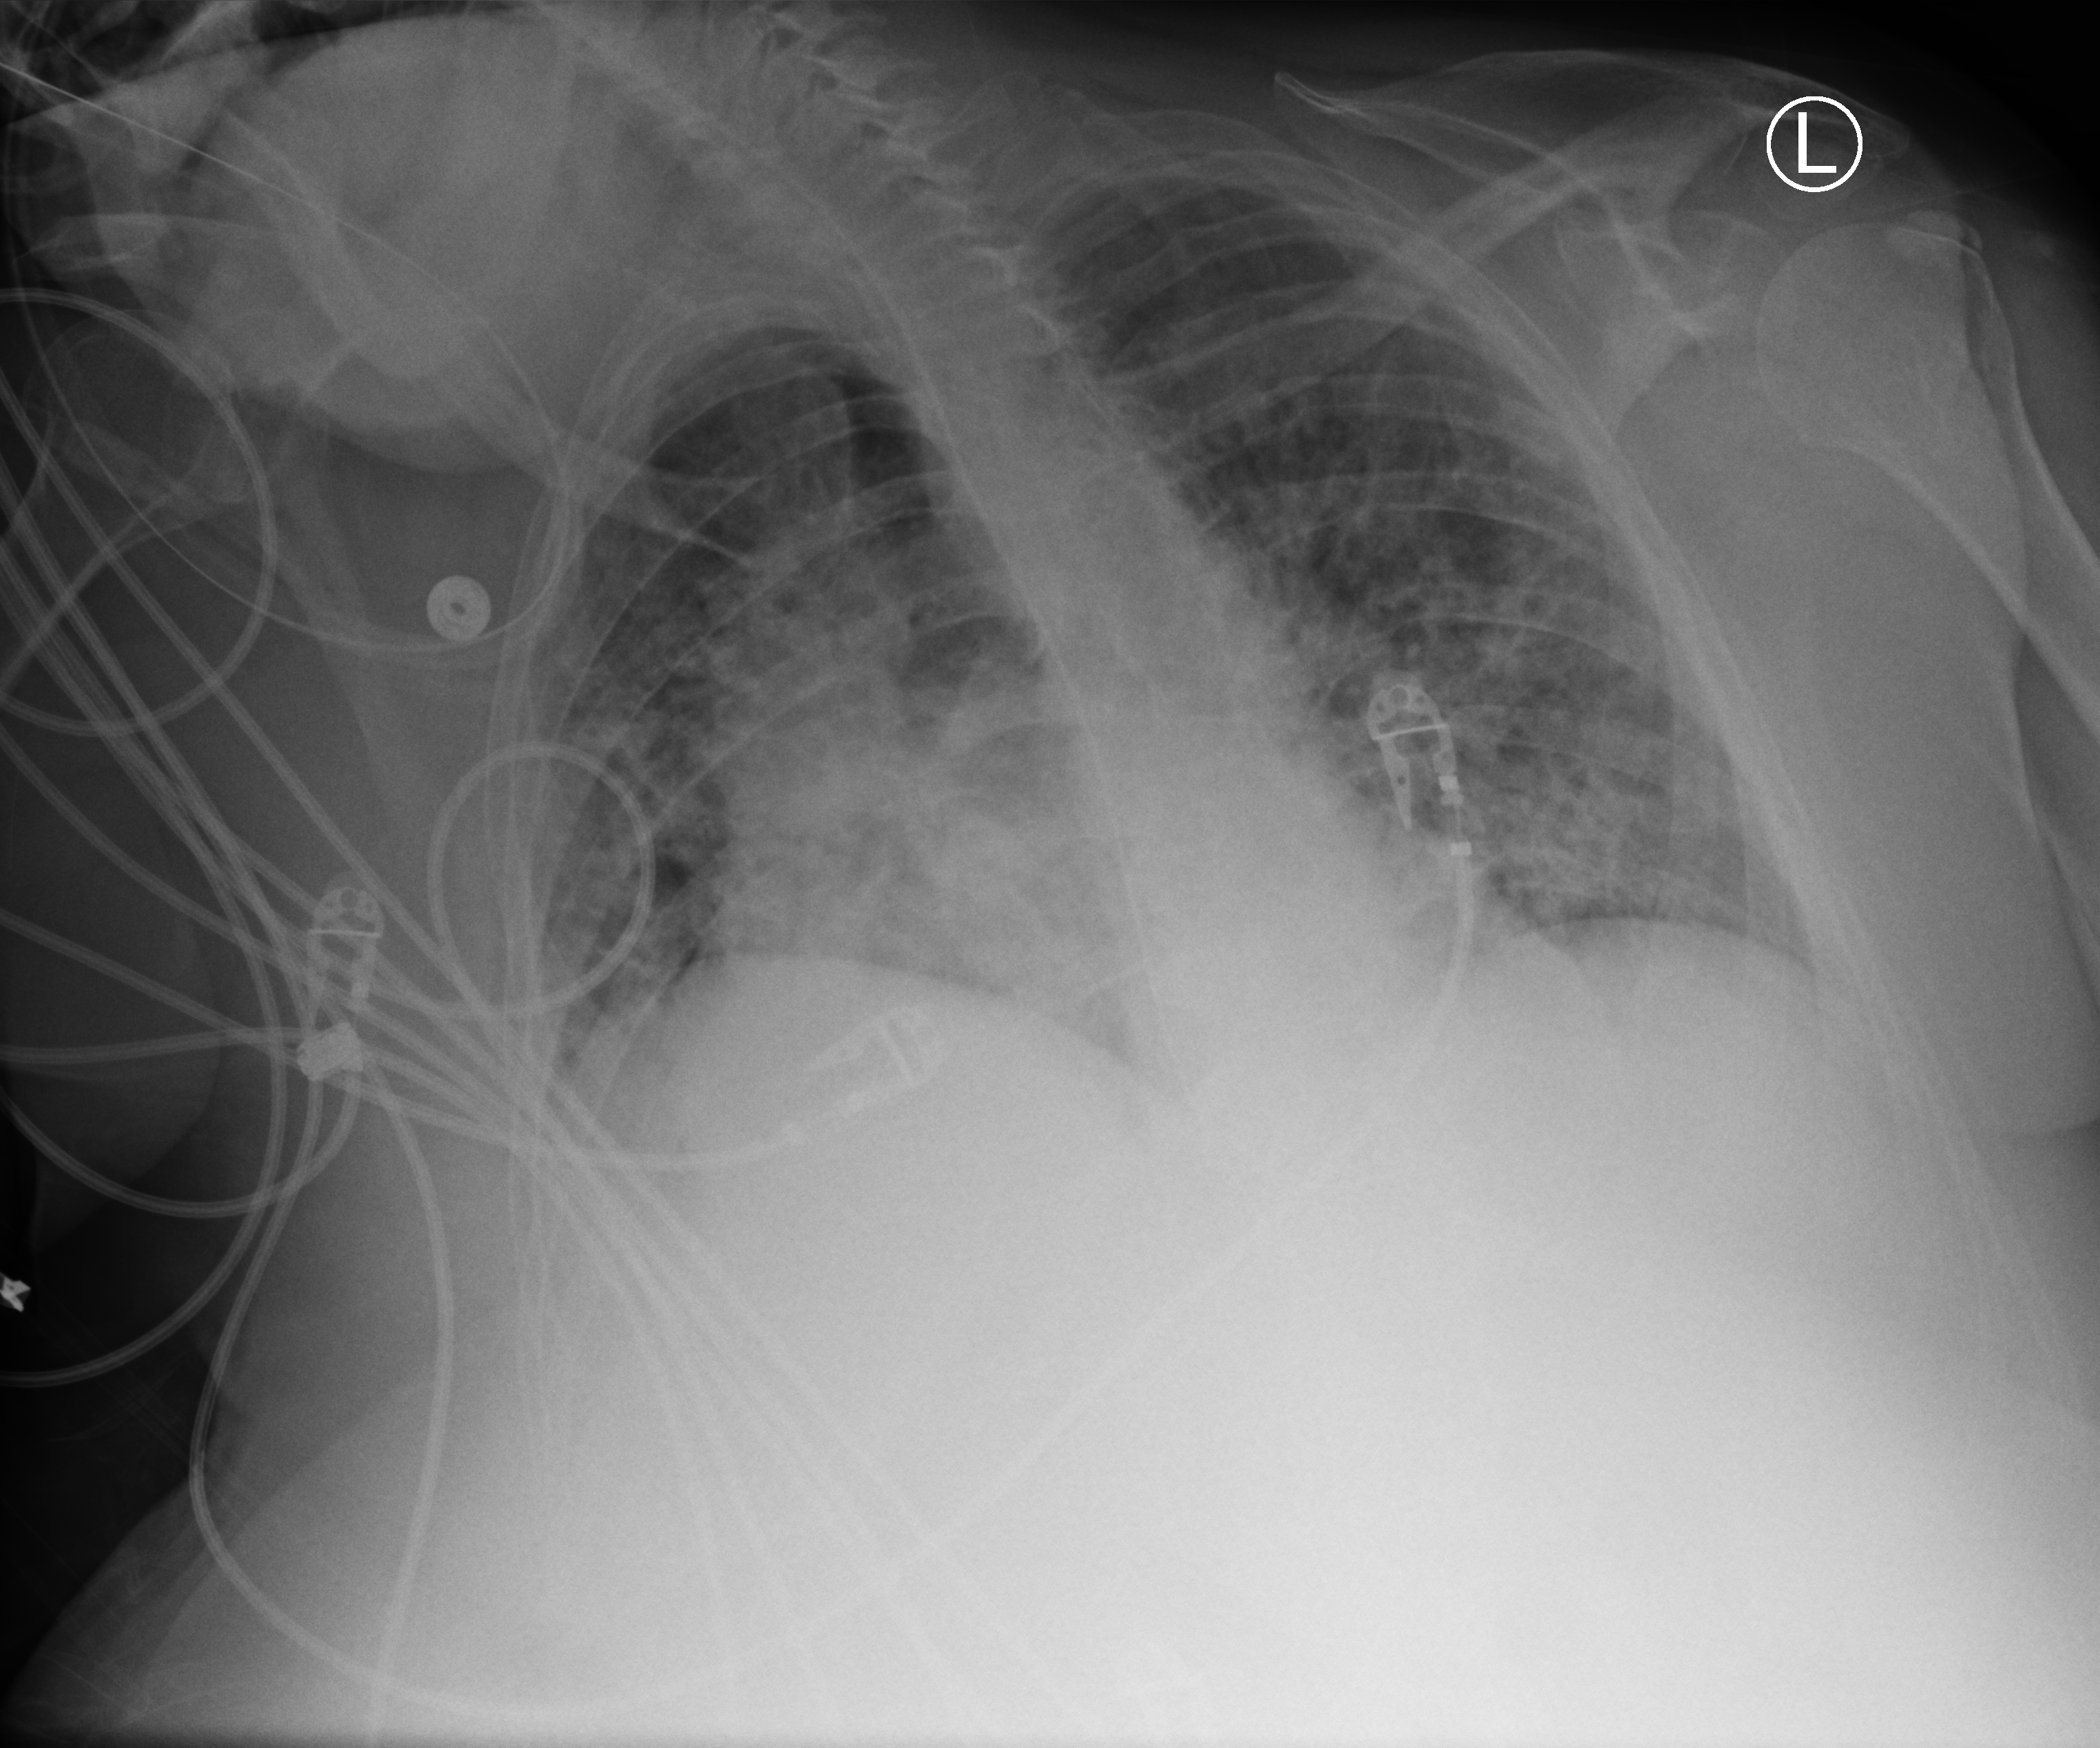
Chest X-ray (portable), anteroposterior (AP) projection. Female patient hospitalised with COVID-19, age 75–90 years.
Hospital-stay facts (about this admission, not read from this image; timing relative to this image not recorded): mechanically ventilated during this hospital stay: yes; admitted to intensive care during this hospital stay: yes.